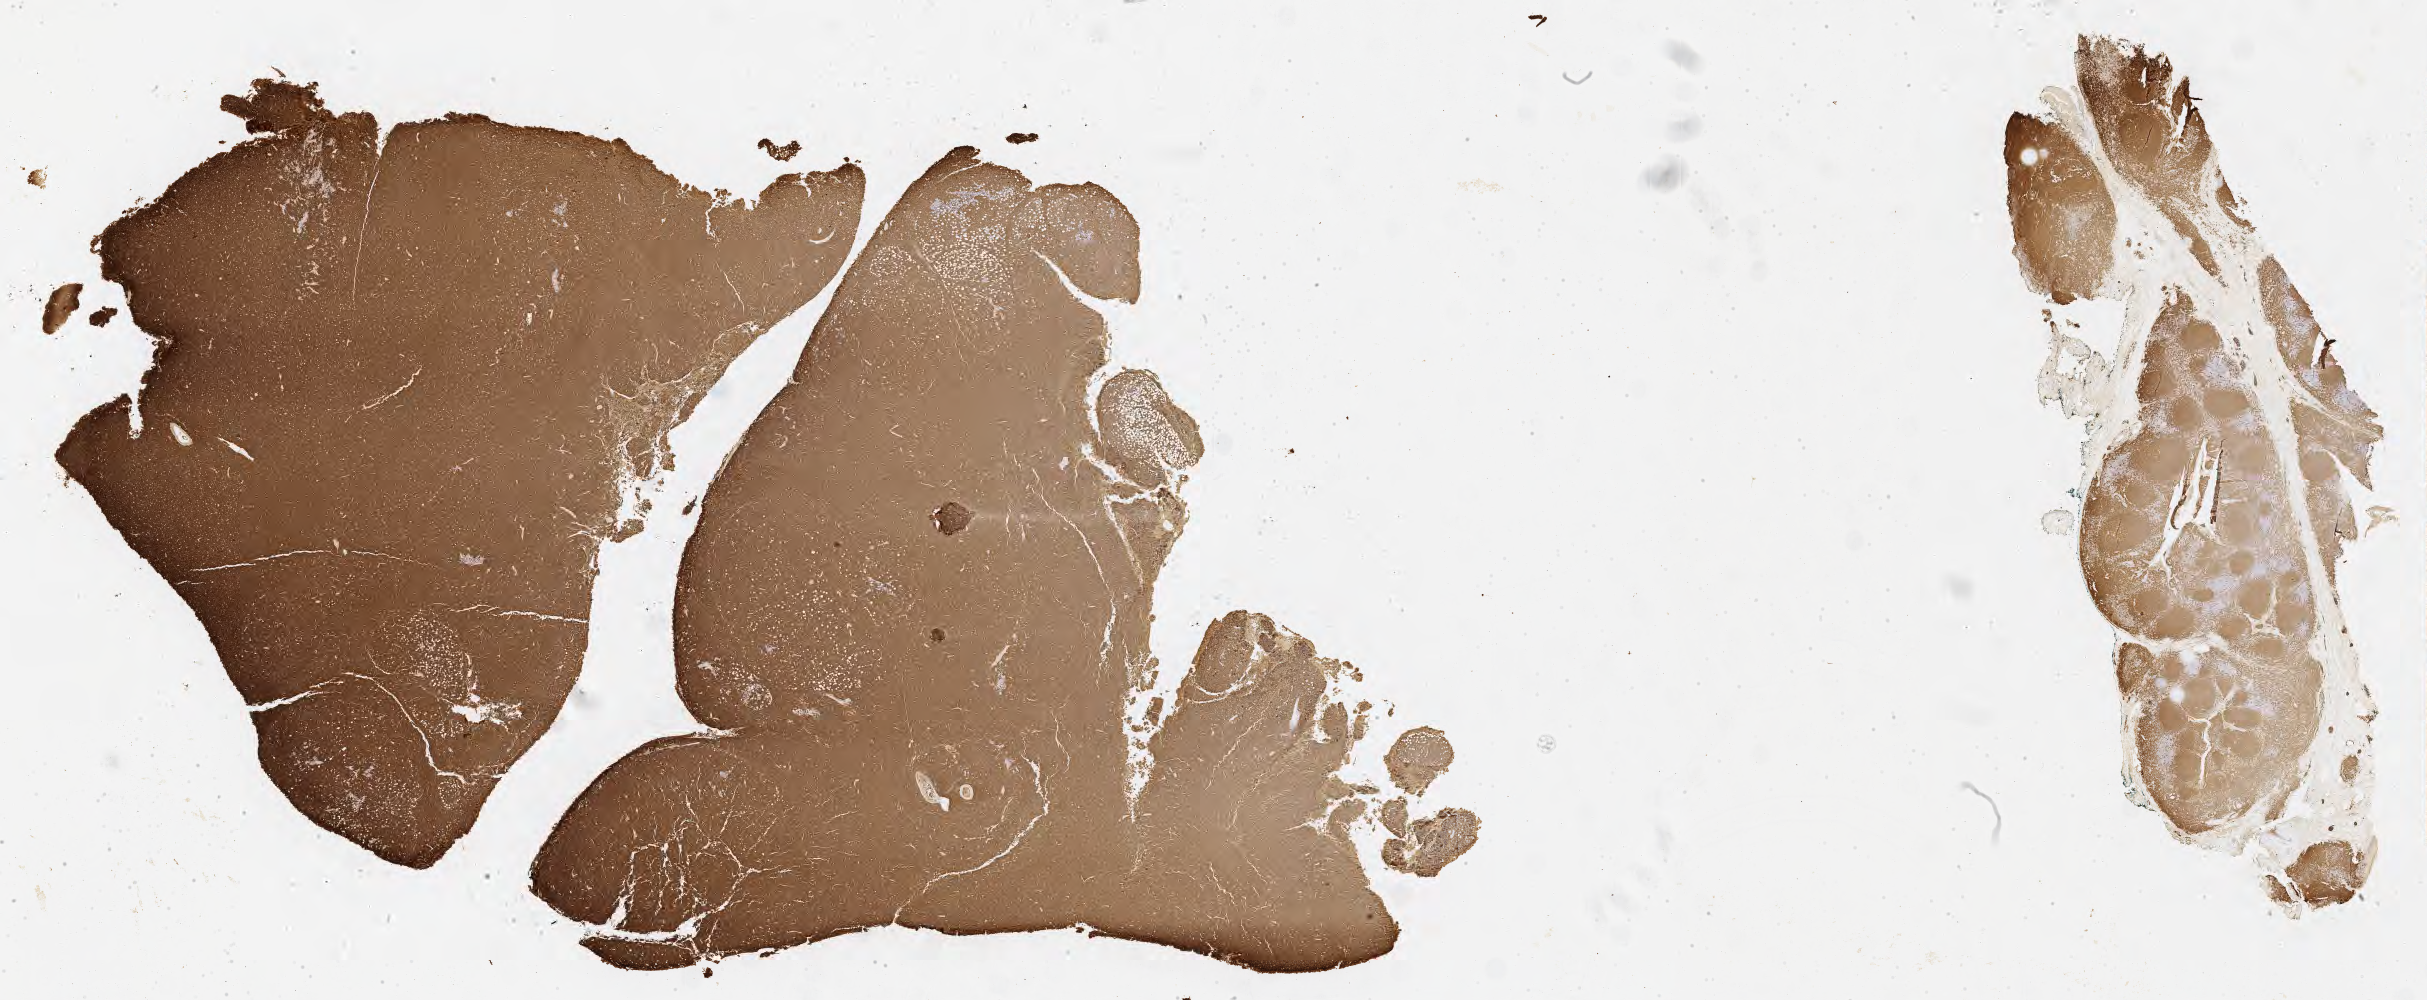
IHC for CD20, whole-slide image, a low-resolution overview of the entire scanned area, about 39.2 x 16.2 mm; specimen: tumor tissue; anatomic site: peritoneum. Male, age 9 years at initial diagnosis.
Histologic diagnosis: Burkitt lymphoma, NOS.